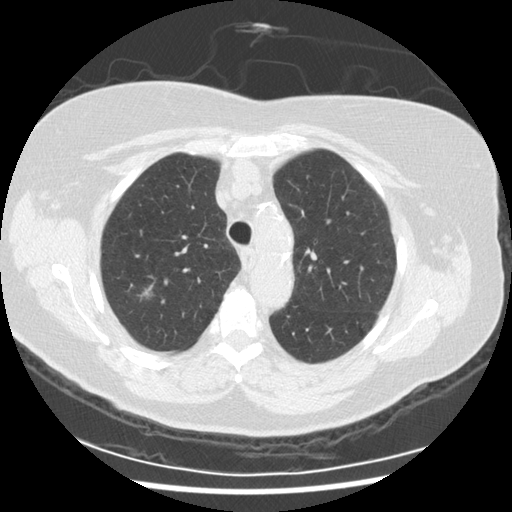
Low-dose screening chest CT, one axial slice. 120 kVp. Lung window (W 1500 / L -600 HU). 2.5 mm slice thickness. 512 × 512 image matrix, field of view 360 × 360 mm.
Structures marked on this image (manually delineated by an expert):
- lesion 1 (tumor, upper lobe of right lung): box from (x=140, y=286) to (x=153, y=297) px